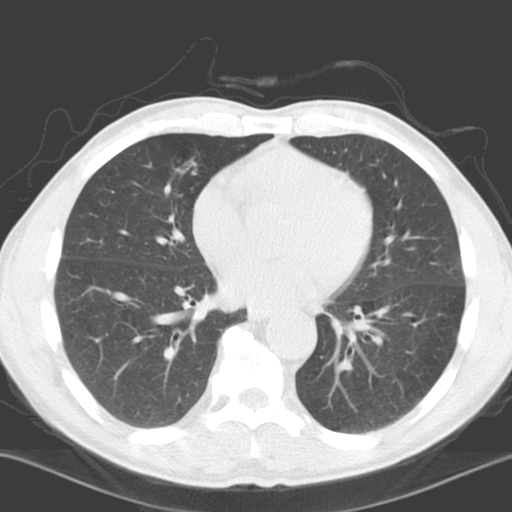
Low-dose screening chest CT, axial slice, first (baseline) screen, lung window (W 1500 / L -600 HU), standard (soft-tissue) reconstruction kernel (C). Male, age 65 years at enrolment. Current smoker at enrolment.
Expert reader's lesion annotation, box from (x=147, y=152) to (x=206, y=216) px. The exam's reader record, not a measurement of the box and not confirmed to be the same lesion: non-calcified nodule or mass ≥4 mm, right lower lobe, 5 × 5 mm, poorly defined margins, soft tissue attenuation. Participant outcome: lung cancer diagnosed 1144 days after this screen (after the third annual screen) — squamous cell carcinoma, NOS, right middle lobe, poorly differentiated (G3), stage IA (AJCC 6th edition), 23 mm at pathology.